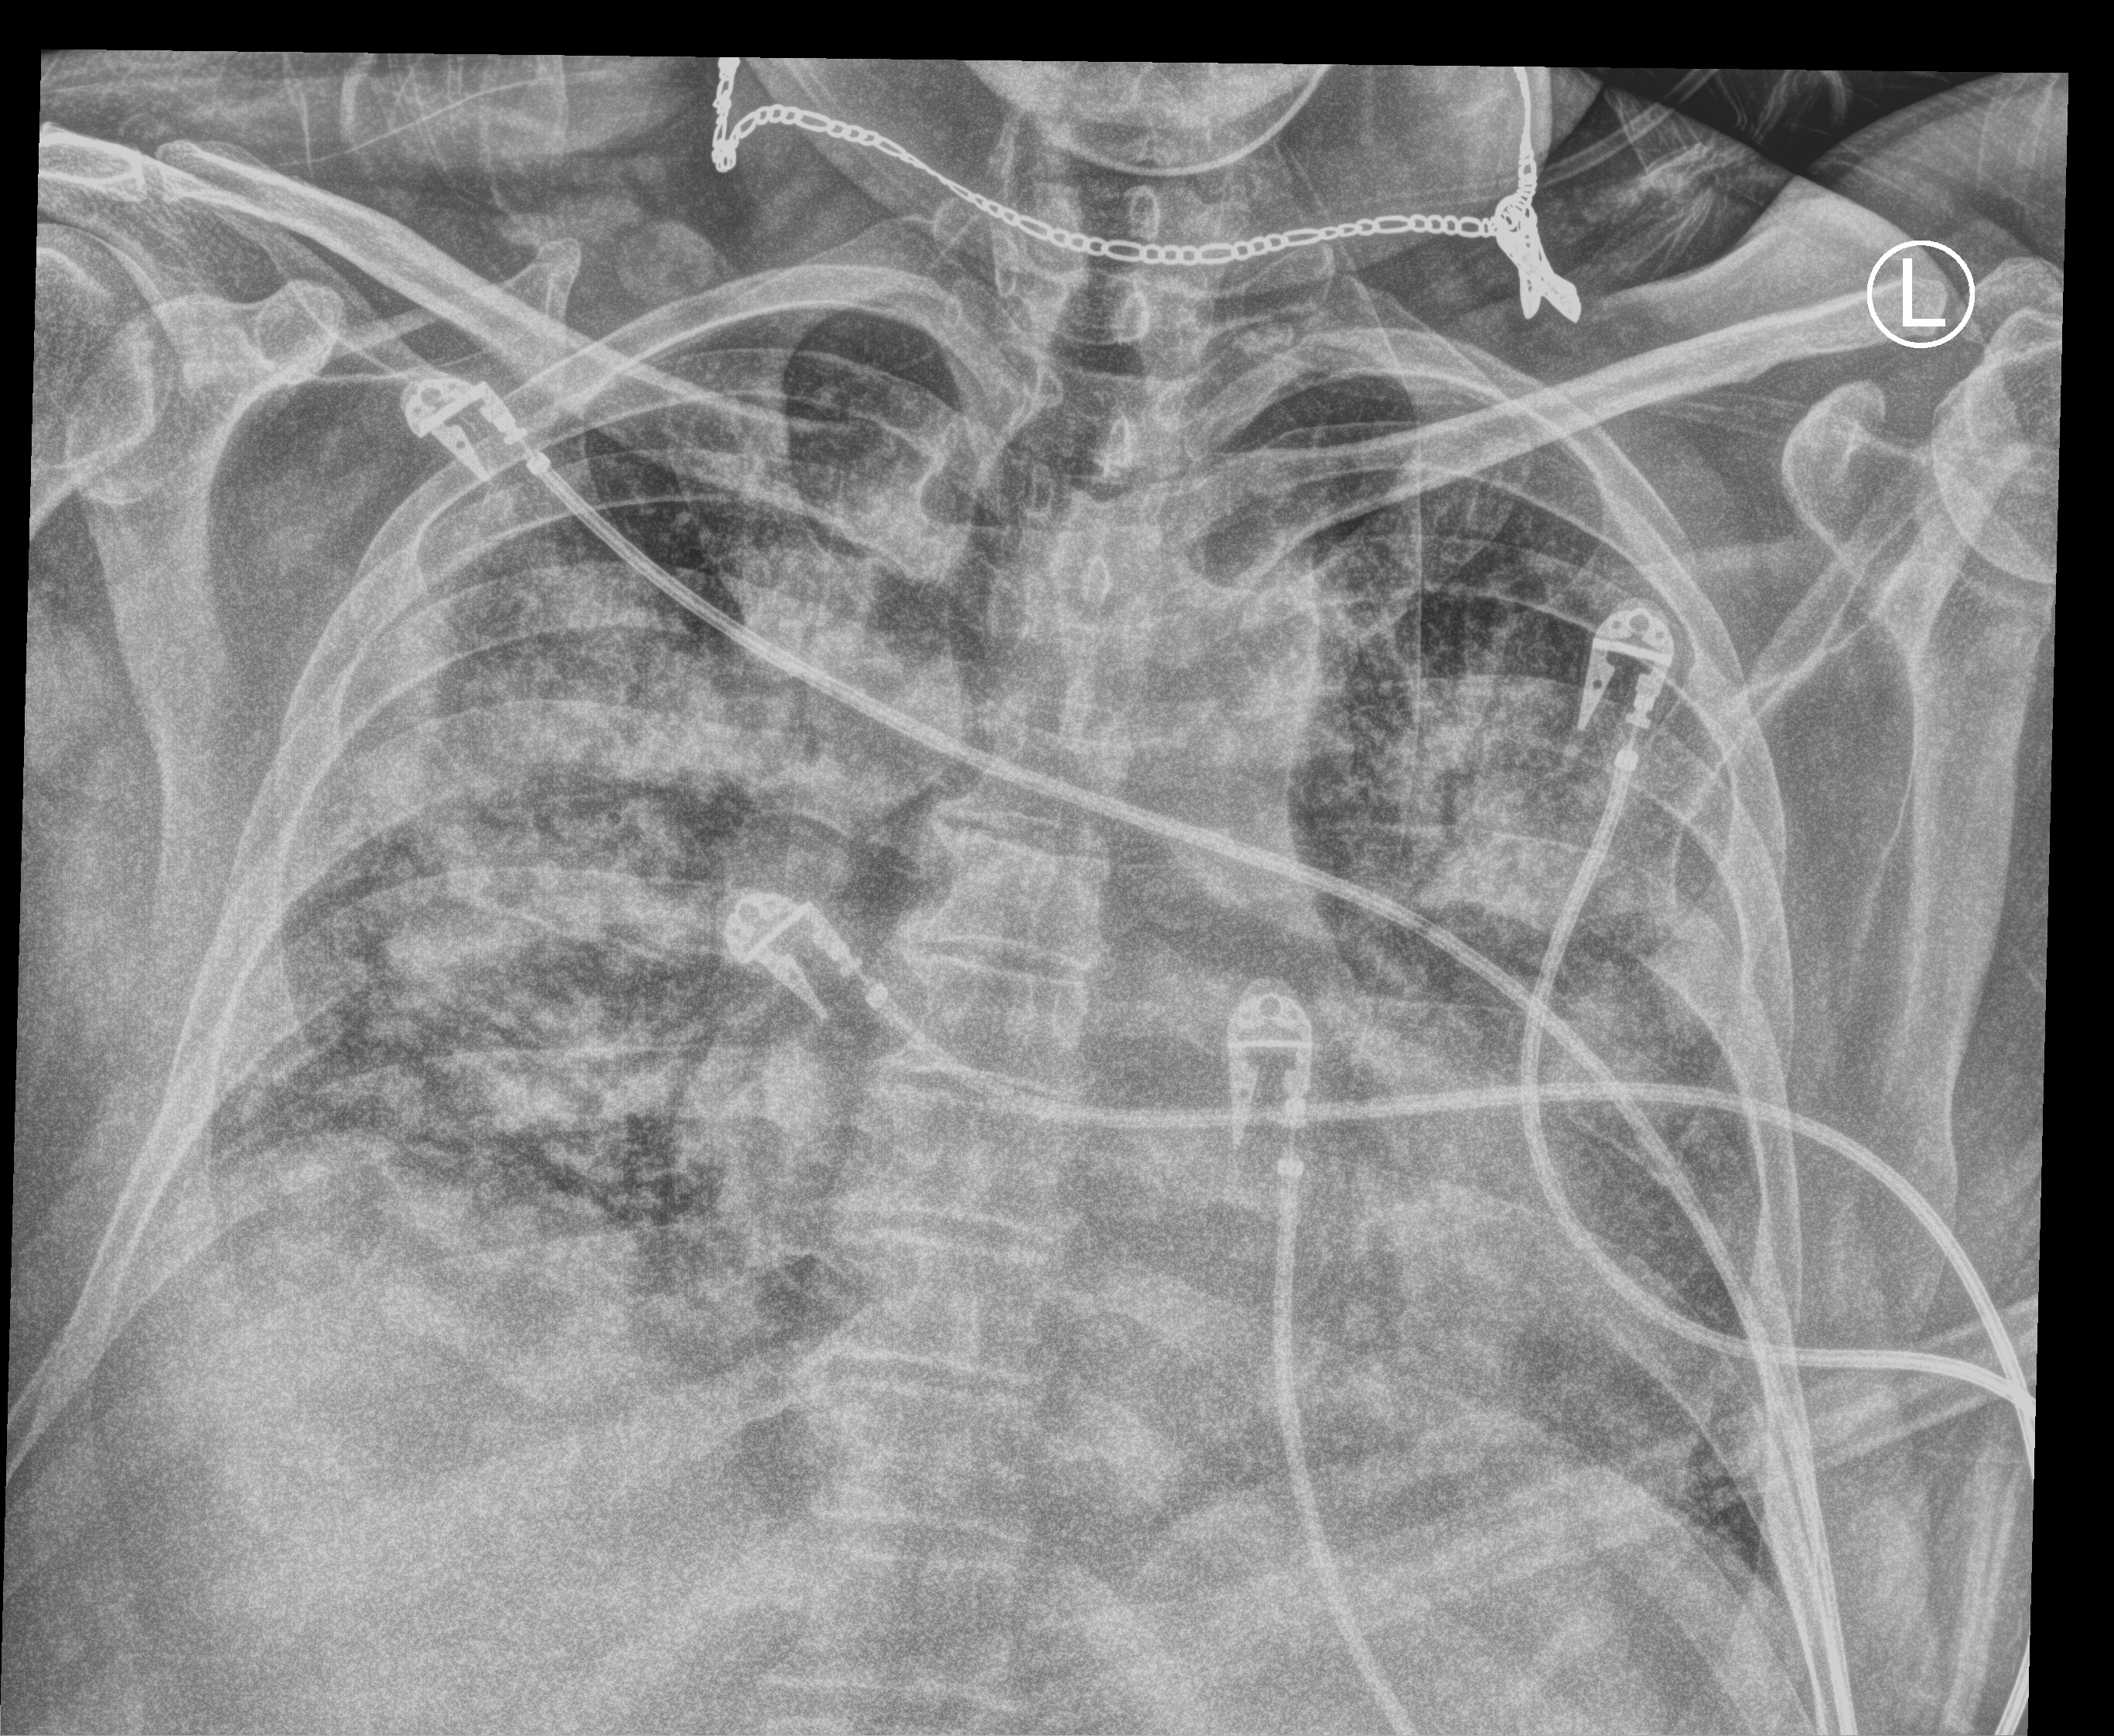
Bedside chest radiograph (computed radiography), anteroposterior (AP) projection. Male patient hospitalised with COVID-19, age 18–59 years.
From the hospital-stay record, not from the radiograph (when in the stay this image was taken is not recorded):
- mechanically ventilated during this hospital stay: yes
- admitted to intensive care during this hospital stay: yes